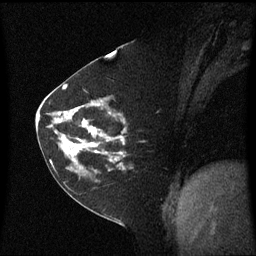
Breast MRI (dynamic contrast-enhanced), one sagittal slice; slice 32 of 60 in the series (ordered by position); dynamic contrast-enhanced series, image 2 of 3 at this slice position (ordered by acquisition); 1.5 T; TE 4.2 ms, TR 8.4 ms; 256 × 256 image matrix, field of view 210 × 210 mm. Patient: female, 60 years. Case-level facts recorded for this patient, not image findings: setting: breast cancer imaged before/during neoadjuvant chemotherapy; receptor status: triple-negative.
Annotated regions visible in this slice (semi-automatic segmentation, software-assisted and operator-edited):
- analysis volume of interest (the breast-tissue region the enhancement analysis was run in; not a lesion): bounding box <45,99,129,182> (left, top, right, bottom; pixels)
- tumour enhancement mask (voxels above the 70 % enhancement threshold inside the analysis volume of interest): <55,104,125,166>